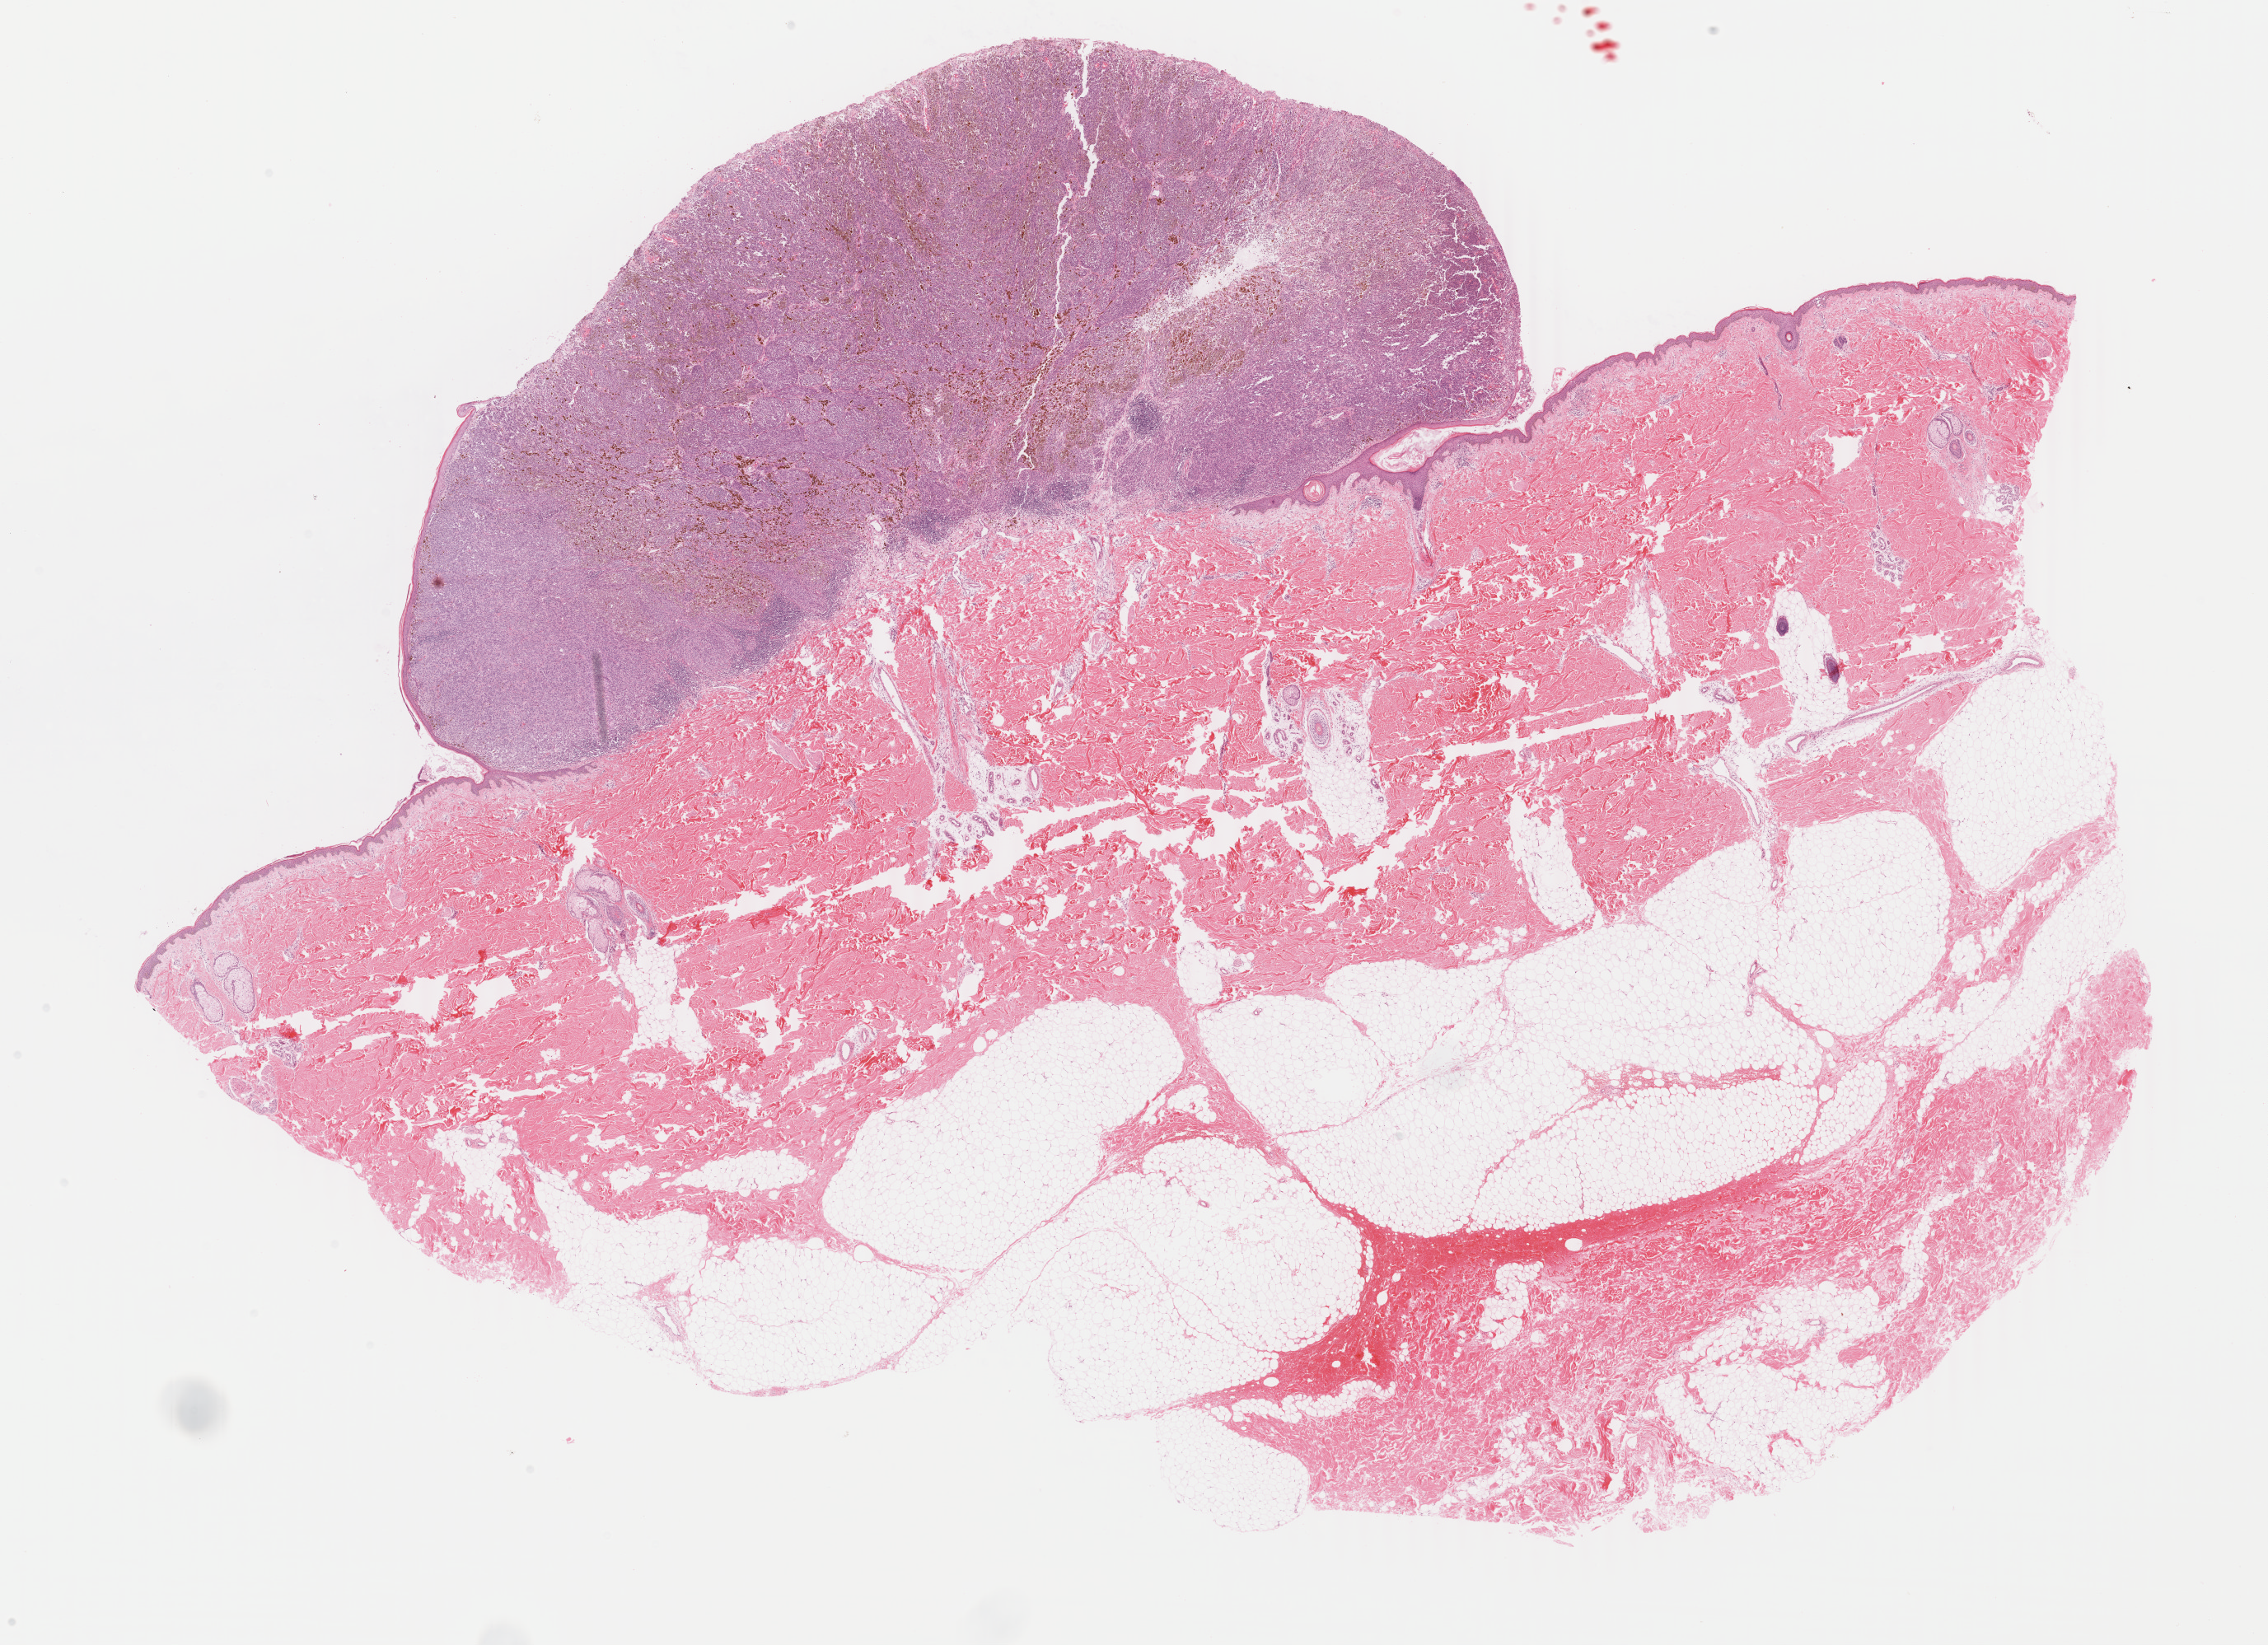
Digitized H&E-stained tissue section (whole slide), whole scanned area (about 21.9 x 15.9 mm, from a 40x scan) shown as a low-resolution overview, formalin-fixed paraffin-embedded (FFPE) diagnostic section, primary tumour sample from the skin. Female, age 48 years at initial diagnosis.
* AJCC pathologic stage: IIC (7th edition)
* diagnosis: Malignant melanoma, NOS